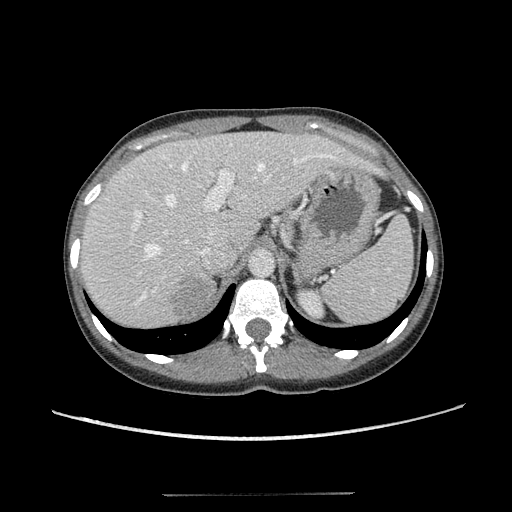
Contrast-enhanced abdominal CT, one axial slice; position 83 of 117 along the scan axis; reconstruction kernel STANDARD; 120 kVp; soft-tissue window (W 400 / L 40 HU); 2.5 mm slice thickness; 512 × 512 image matrix, field of view 365 × 365 mm. Patient: female, 35 years. Case-level facts recorded for this patient, not image findings: diagnosis: adrenocortical carcinoma; tumour side: right adrenal; tumour size at pathology: 3 cm; Ki-67 index: 21 %; stage (as recorded): 3.
Structures marked on this image (semi-automatically segmented with operator editing):
- mass: box from (x=173, y=278) to (x=212, y=314) px